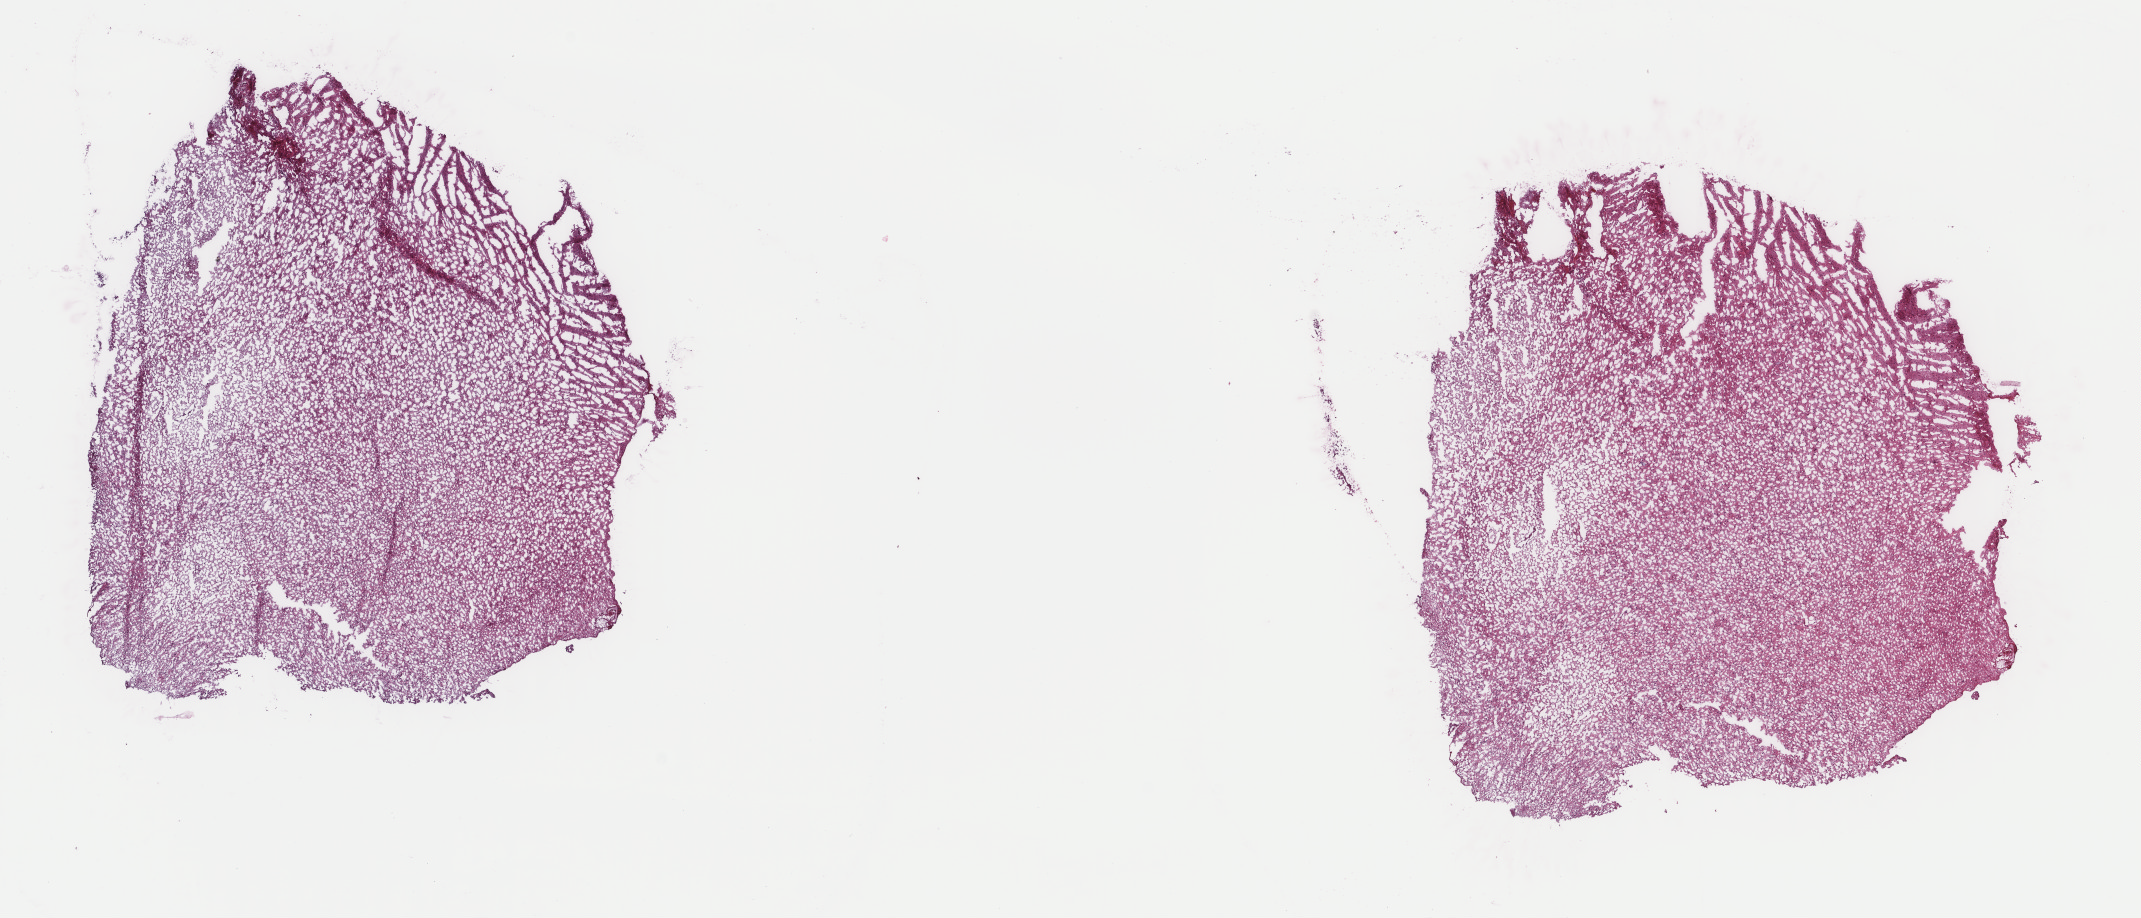
Whole-slide histology image, H&E-stained — whole scanned area (about 17.0 x 7.3 mm, acquisition: 40x scan) shown as a low-resolution overview; frozen section from the top of the tissue portion; brain, primary tumour sample. Female, age 43 years at initial diagnosis. Histologic grade: G2 (moderately differentiated). Slide review estimates, as recorded: tumour cells 60%, tumour nuclei 80%, normal cells 15%, stromal cells 25%, necrosis 0%. Infiltration values recorded for this section: lymphocyte infiltration 0%, monocyte infiltration 0%, neutrophil infiltration 0%.
• diagnosis: Oligodendroglioma, NOS